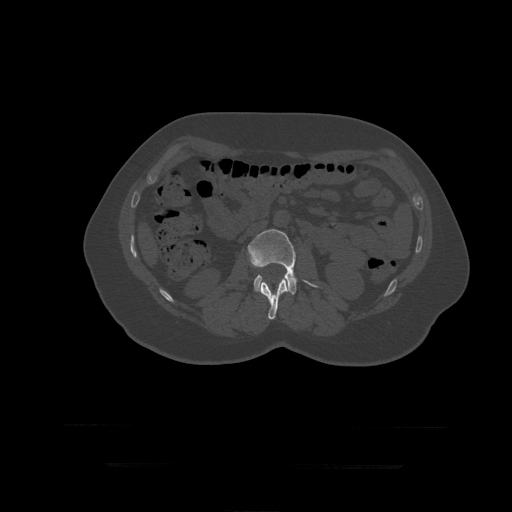
CT including the spine, one axial slice. Position 135 of 399 along the scan axis. 120 kVp. Bone window (W 1800 / L 400 HU). 1.25 mm slice thickness. 512 × 512 image matrix, field of view 450 × 450 mm. Patient age 41 years. Case-level facts recorded for this patient, not image findings: primary cancer: breast.
Annotated regions visible in this slice (semi-automatically segmented with operator editing):
- L2 vertebra: box from (x=260, y=279) to (x=288, y=320) px
- L3 vertebra: (x=248, y=229)–(x=319, y=295)